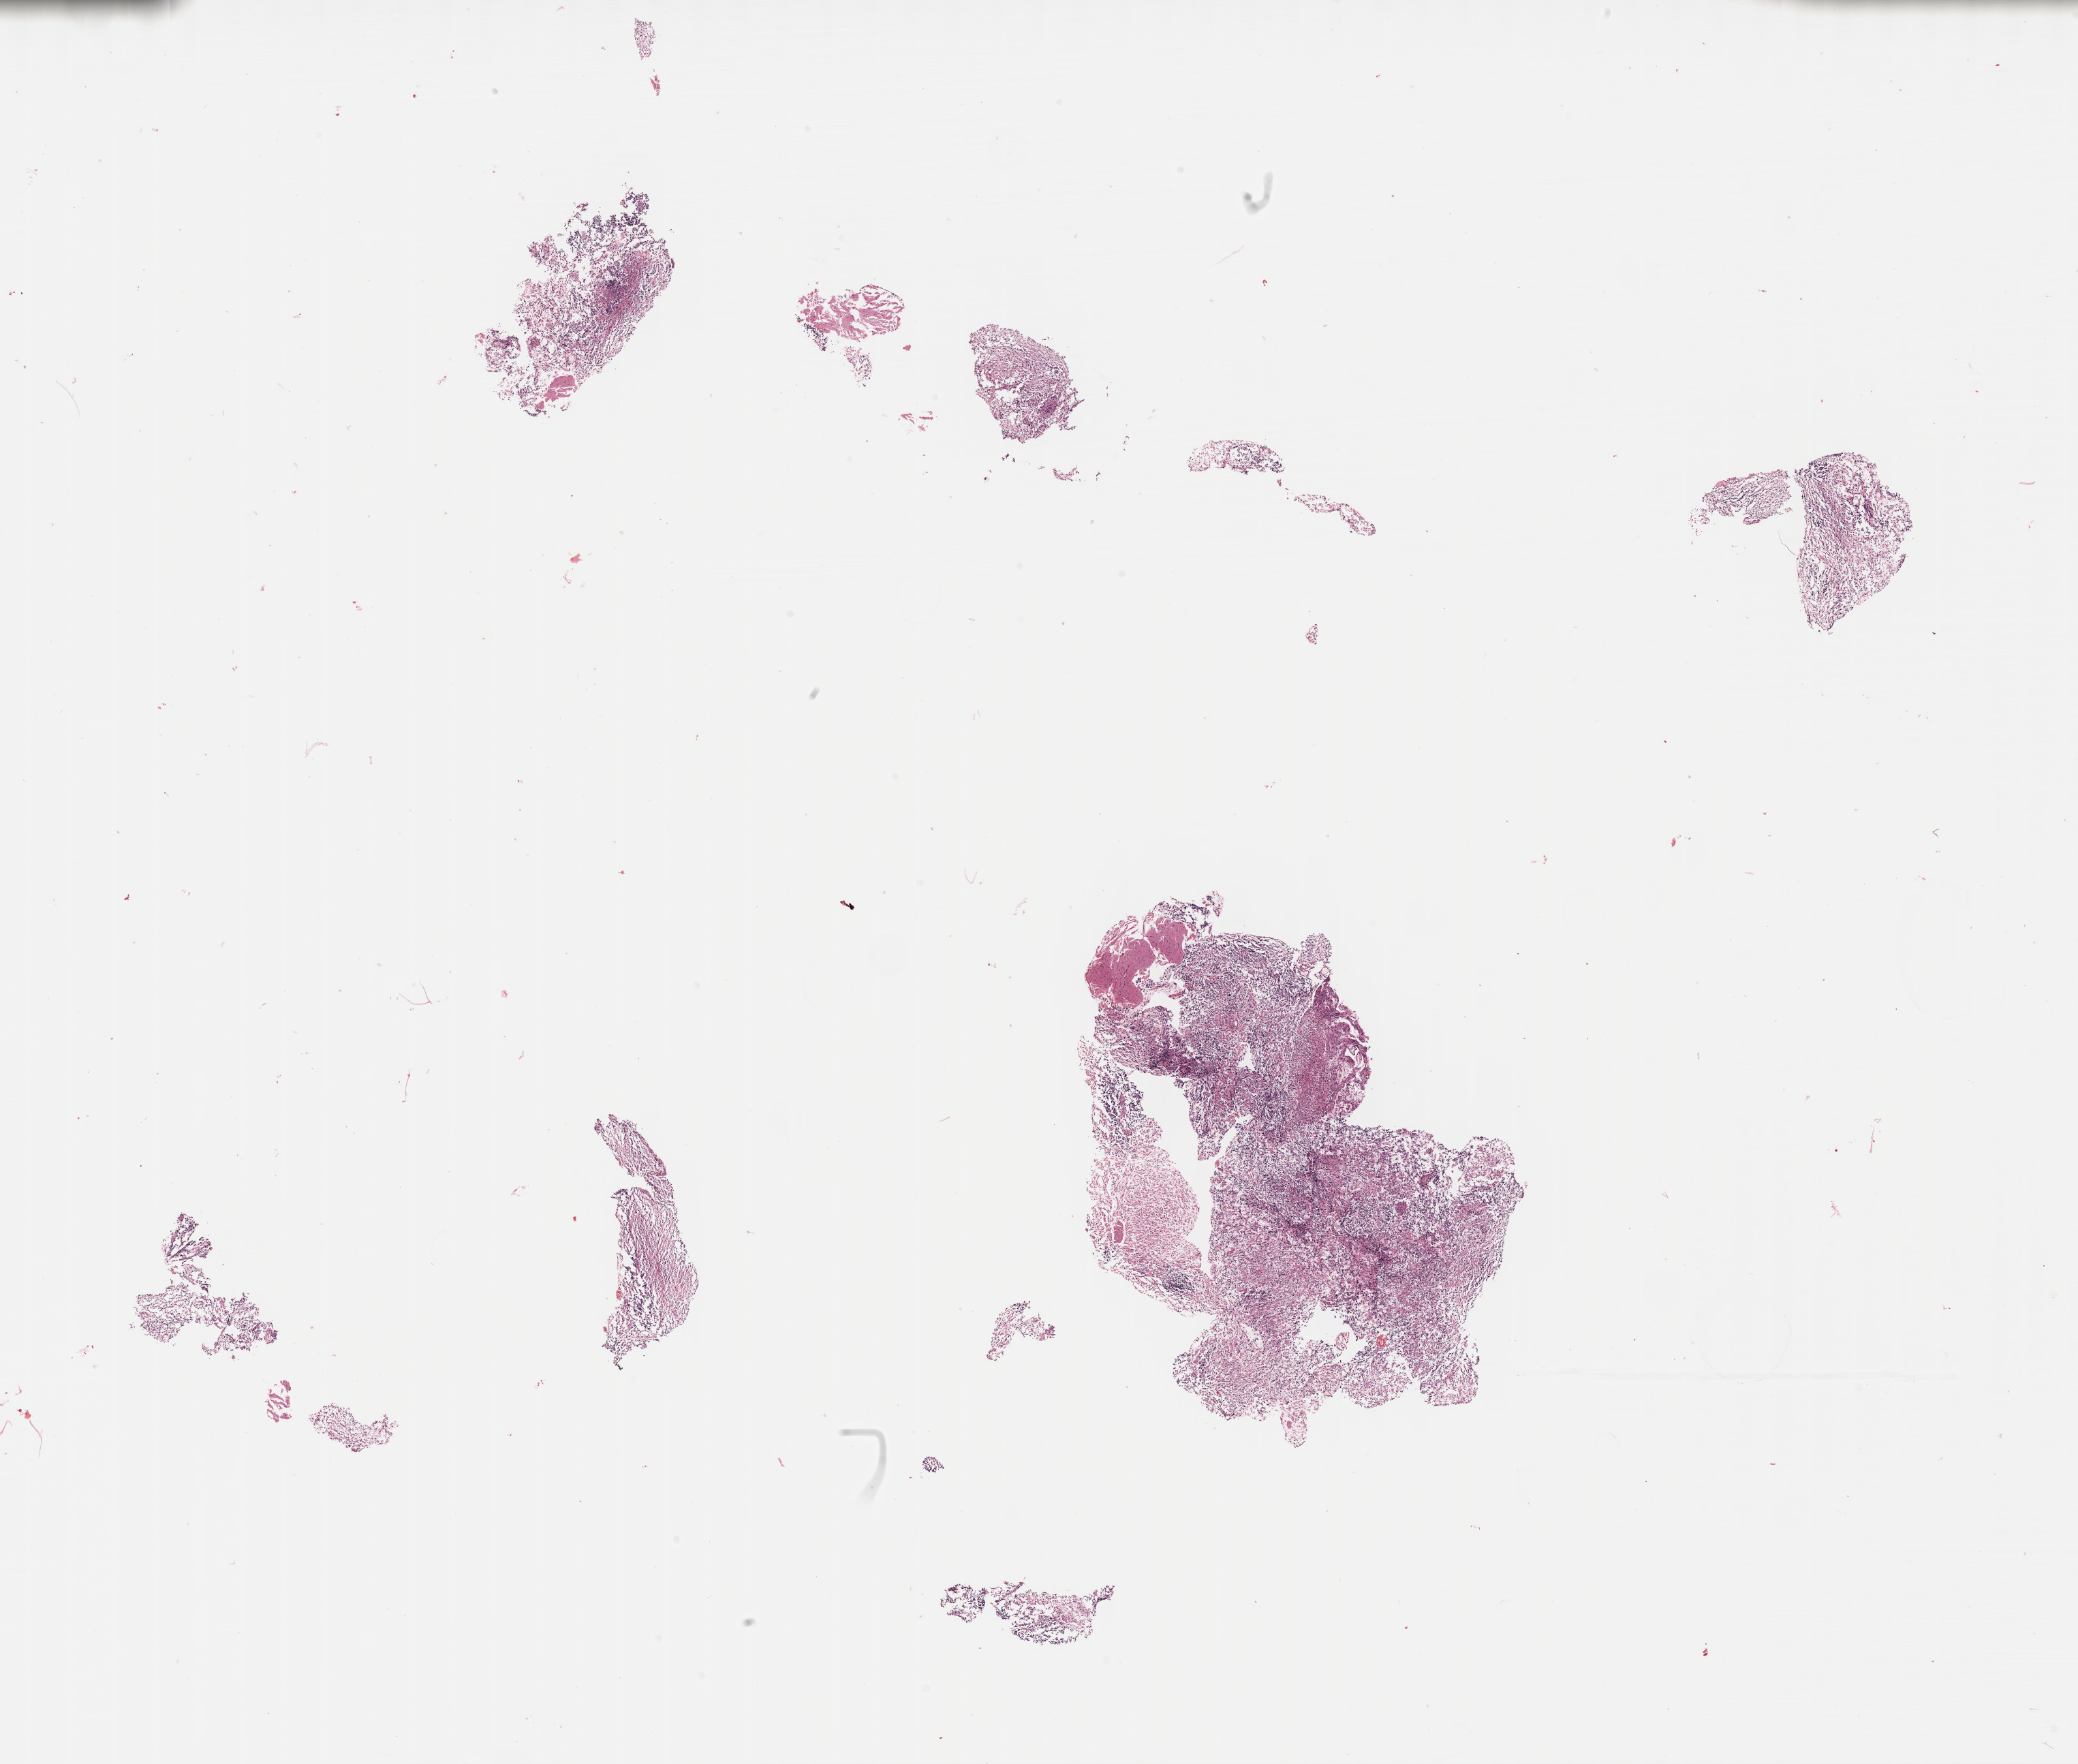
Digitized H&E-stained tissue section (whole slide), low-resolution overview of the scanned area, about 24.7 x 20.9 mm; formalin-fixed paraffin-embedded (FFPE) diagnostic section; primary tumour sample from the brain. Male patient; age at initial diagnosis 30 years.
Pathologic diagnosis: Astrocytoma, anaplastic (cerebrum).